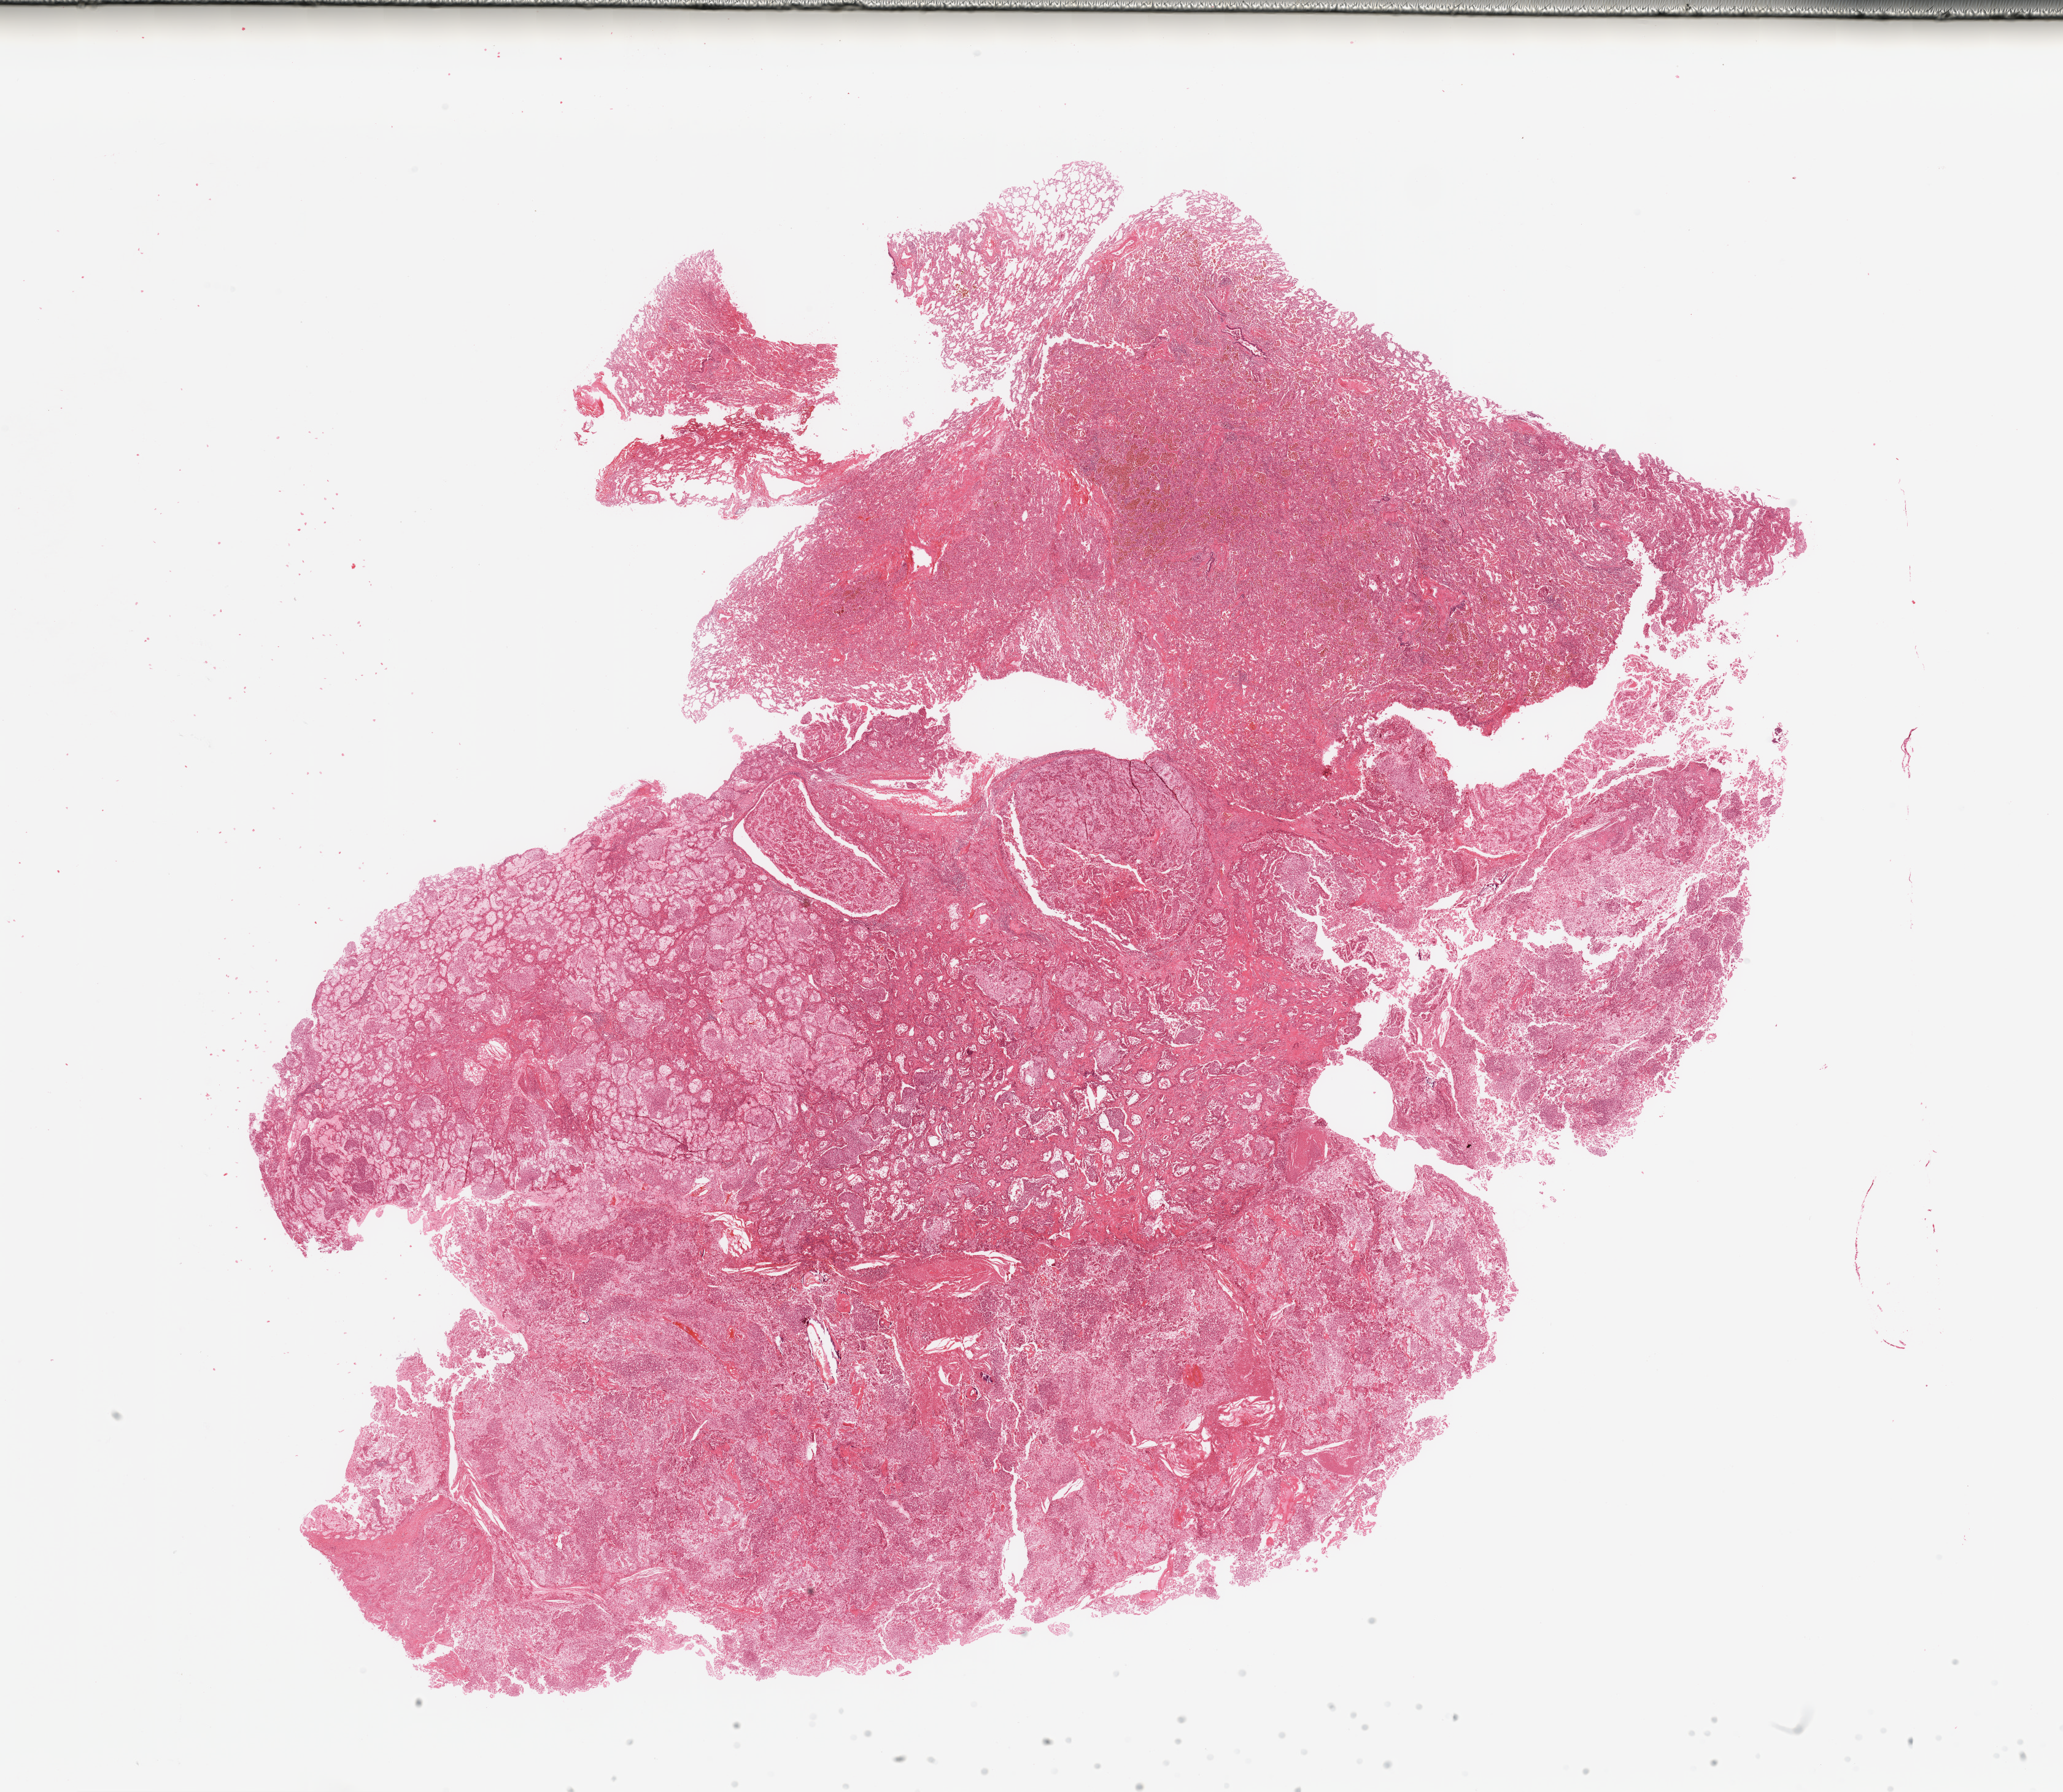
Whole-slide histology image, H&E-stained — shown as a low-resolution overview of the whole scanned area (about 26.6 x 23.1 mm, acquisition: 20x scan). Tumour tissue sample, lung. Patient: female, age 25 years.
Diagnosis: Adenocarcinoma, NOS.